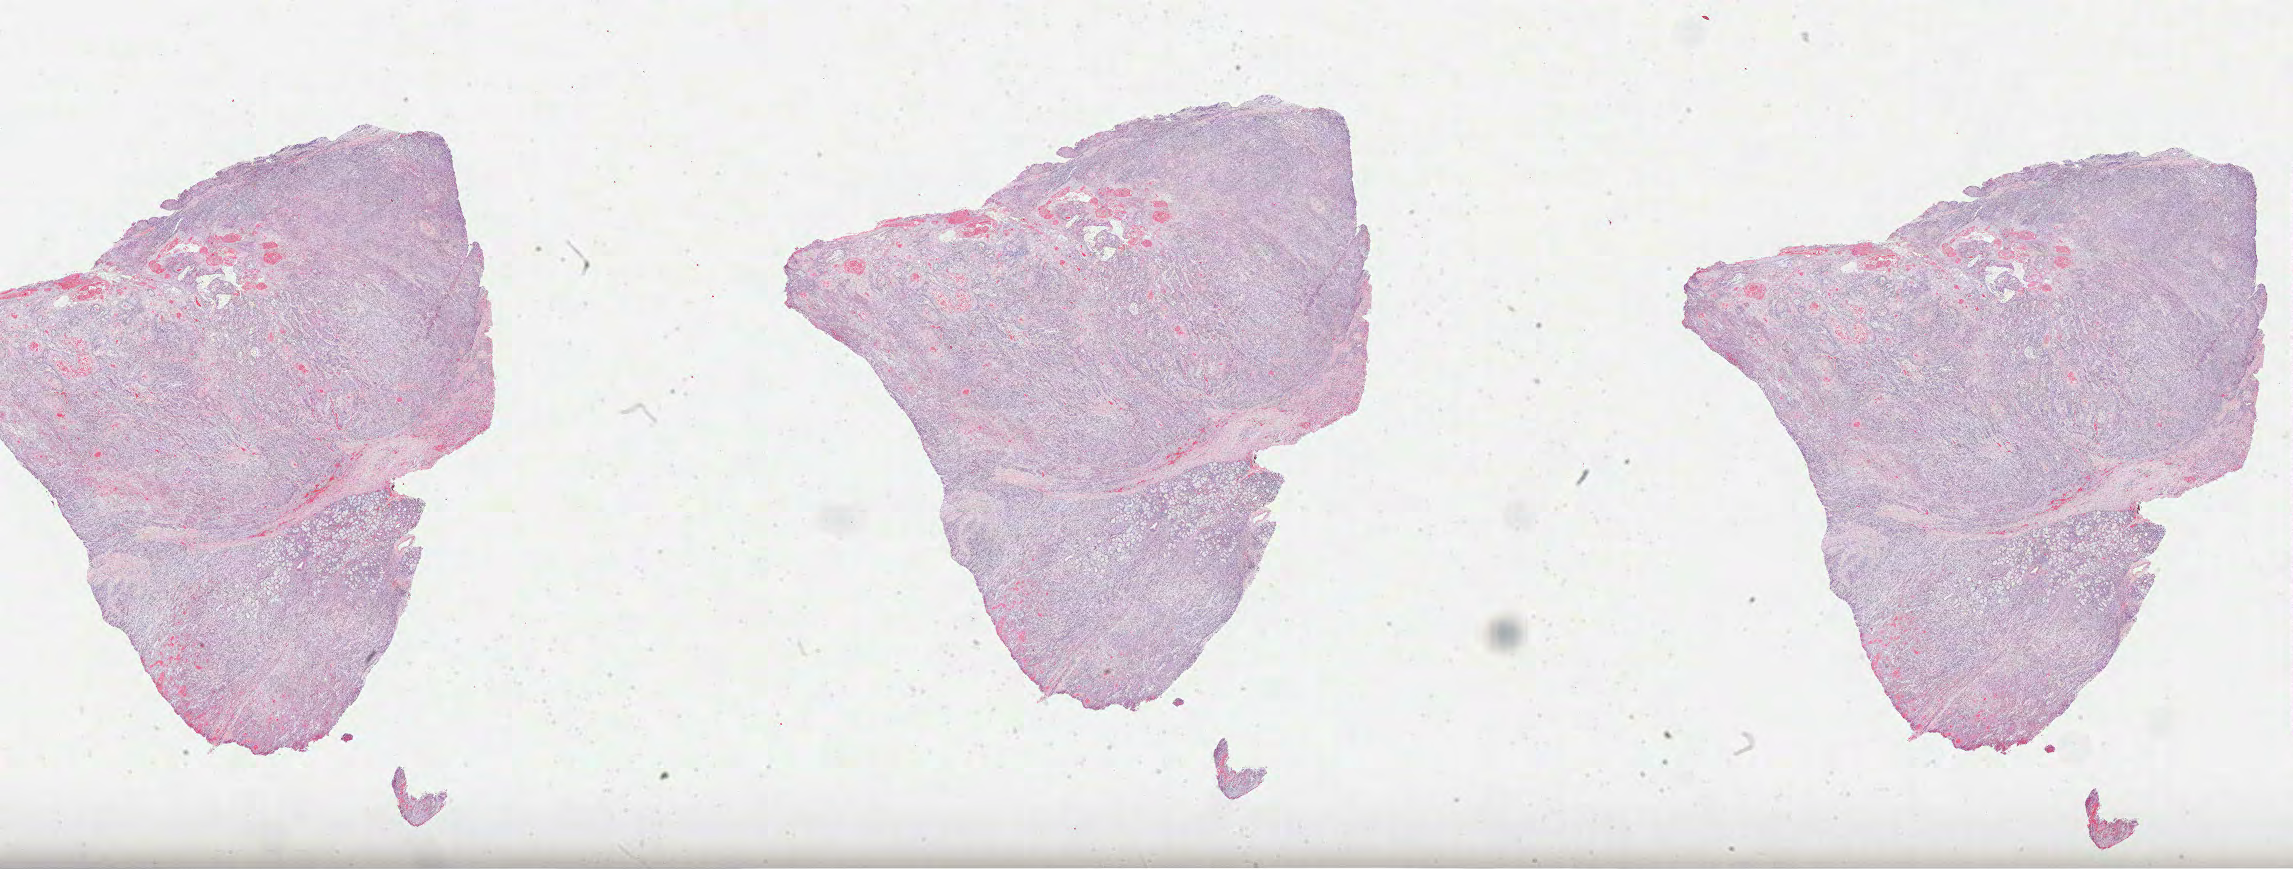
H&E whole-slide image, low-resolution overview of the scanned area, about 37.0 x 14.0 mm (slide scanned at 40x). Formalin-fixed paraffin-embedded (FFPE) diagnostic section. Primary tumour sample from the head and neck. Patient: male, age at initial diagnosis 57 years. Histologic grade: G3 (poorly differentiated).
- TNM: T4a N0
- pathologic diagnosis: Squamous cell carcinoma, NOS (gum, NOS)
- AJCC pathologic stage: IVA (7th edition)
- lymph nodes positive (case pathology): 0 of 44 examined